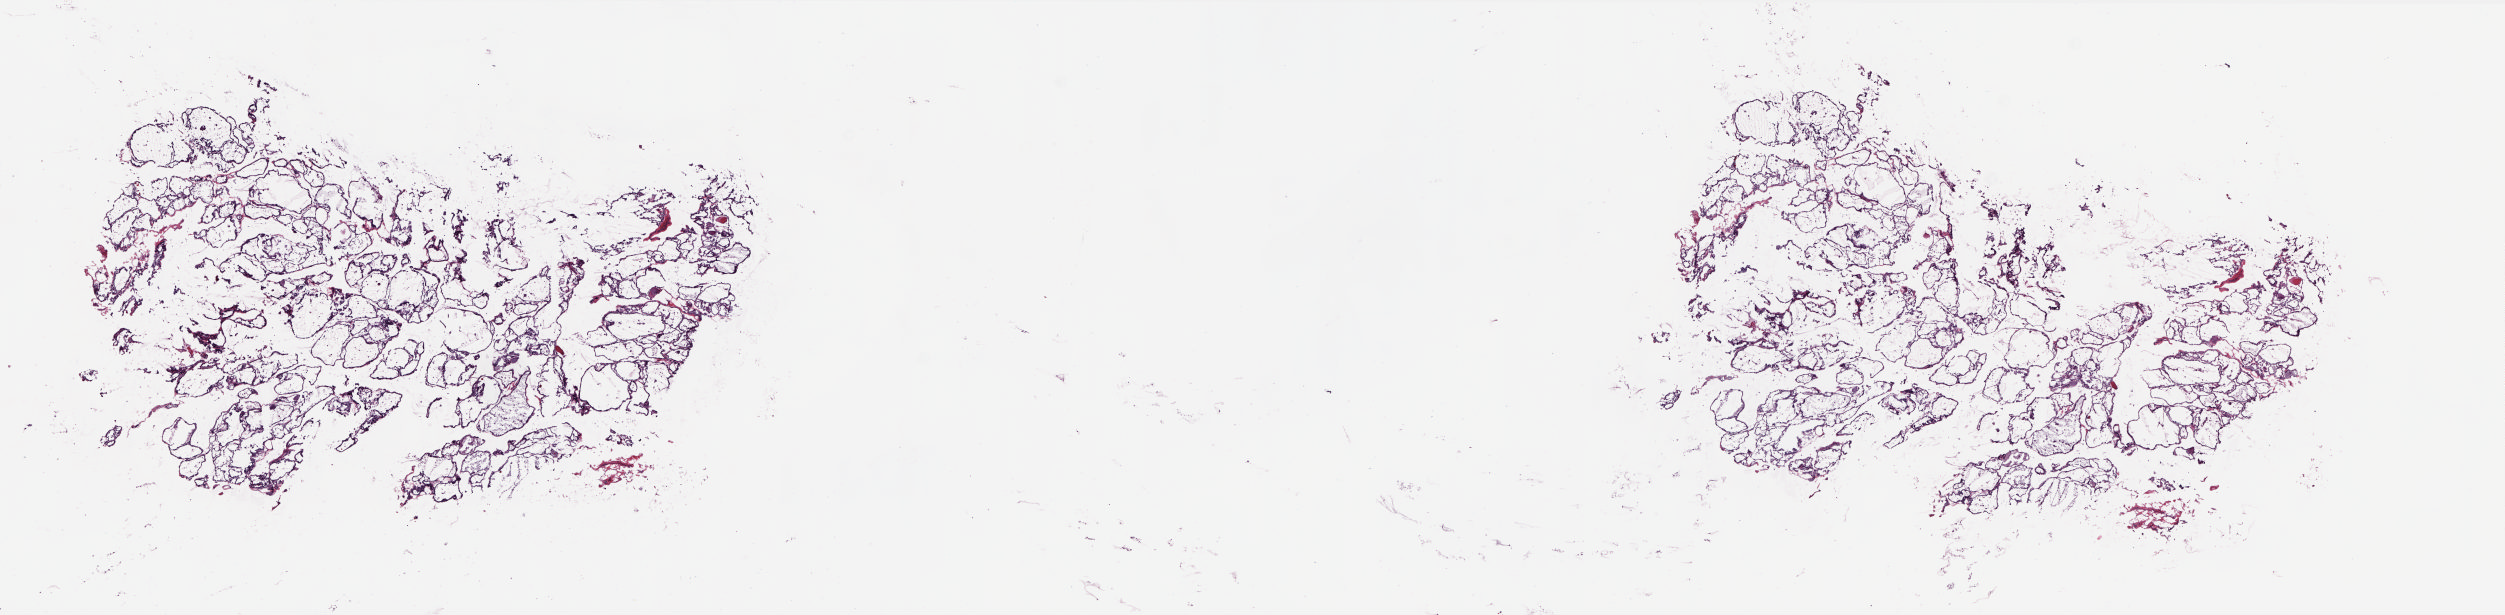
H&E-stained whole-slide image, a low-resolution overview of the entire scanned area, about 20.2 x 5.0 mm; frozen section from the top of the tissue portion; thyroid, solid tissue normal (non-tumour tissue) sample. Patient: male, age at initial diagnosis 75 years. Slide review estimates, as recorded: tumour cells 0%, tumour nuclei 0%, normal cells 100%, stromal cells 0%, necrosis 0%. Infiltration values recorded for this section: lymphocyte infiltration 3%, monocyte infiltration 3%, neutrophil infiltration 0%.
- this section: solid tissue normal sample (biorepository sample class)
- patient diagnosis: Papillary adenocarcinoma, NOS (thyroid gland)